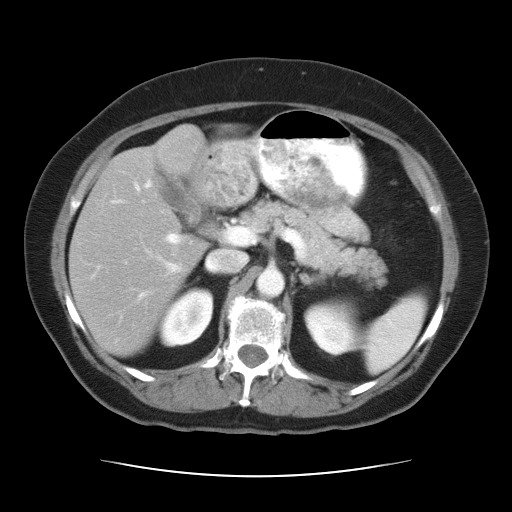
Contrast-enhanced abdominal CT, one axial slice. Slice 18 of 34 in the series (ordered by position). Reconstruction kernel STANDARD. 120 kVp. Intravenous contrast given. Soft-tissue window (W 400 / L 40 HU). 512 × 512 image matrix, field of view 360 × 360 mm. Female patient, age 65 years. From the clinical record (not read from this slice): diagnosis: colorectal cancer liver metastases, imaged before liver resection; multiple liver metastases: yes; largest metastasis: 2.2 cm.
Outlined on this slice (manually delineated by an expert):
- hepatic veins: box from (x=134, y=179) to (x=247, y=271) px
- liver: (x=70, y=131)–(x=203, y=354)
- planned liver remnant (the part of the liver to remain after resection): (x=70, y=133)–(x=203, y=354)
- portal vein (with intrahepatic branches): (x=140, y=225)–(x=228, y=297)